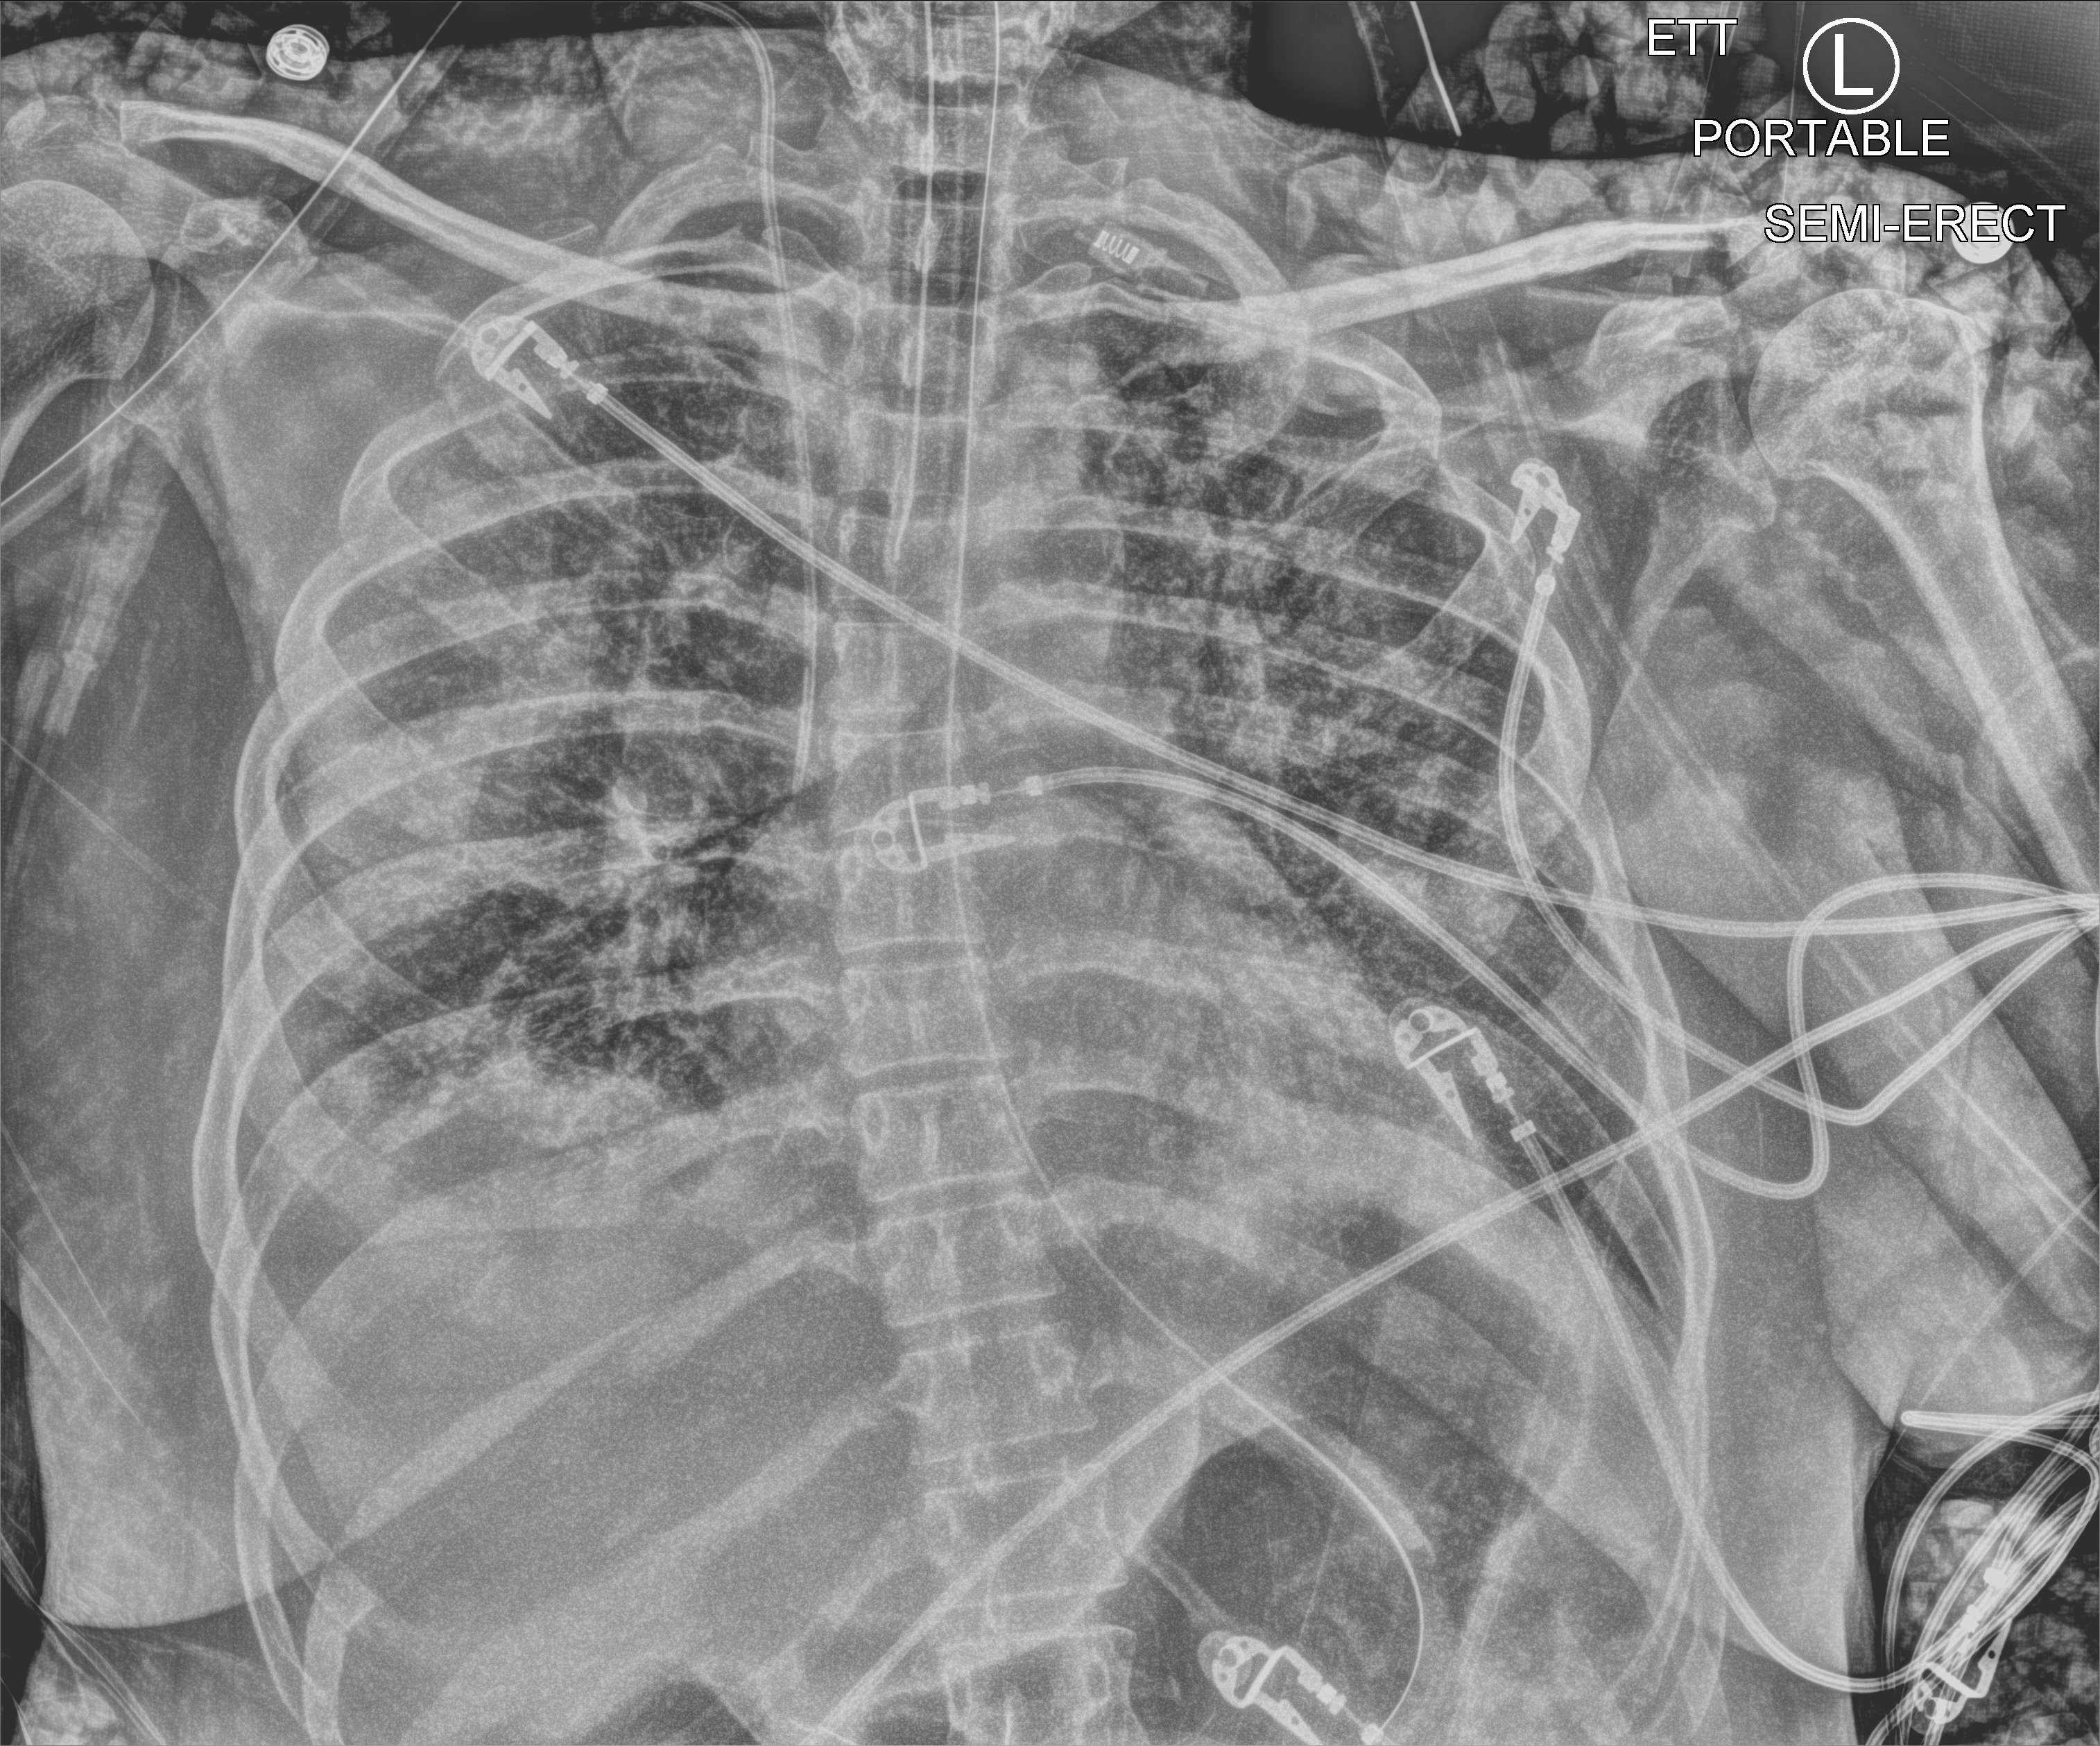
Bedside chest radiograph (computed radiography). Patient hospitalised with COVID-19, aged 18–59 years.
Admission-level facts for this patient (not findings on this image; timing relative to this image not recorded):
- mechanically ventilated during this hospital stay: yes
- other chronic lung disease (admission record): no